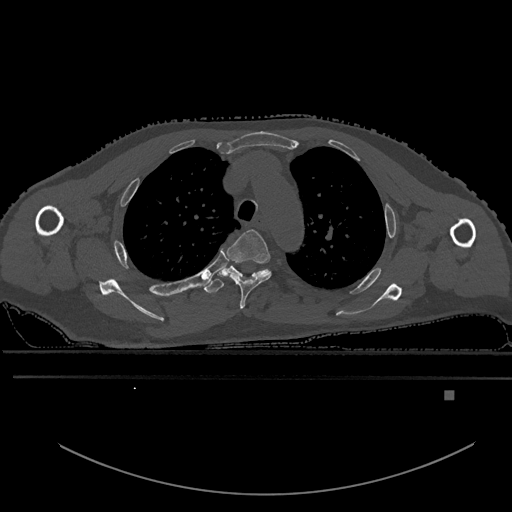
CT including the spine, one axial slice. Slice 435 of 969 in the series (ordered by position). Bone window (W 1800 / L 400 HU). 512 × 512 image matrix, field of view 456 × 456 mm. Male patient, age 82 years. From the clinical record (not read from this slice): primary cancer: prostate; vertebrae with lytic lesions (as recorded): T11, T9, T8, T2.
Structures marked on this image (semi-automatic segmentation, software-assisted and operator-edited):
- T3 vertebra: box from (x=227, y=229) to (x=272, y=309) px
- T4 vertebra: (x=203, y=264)–(x=271, y=294)